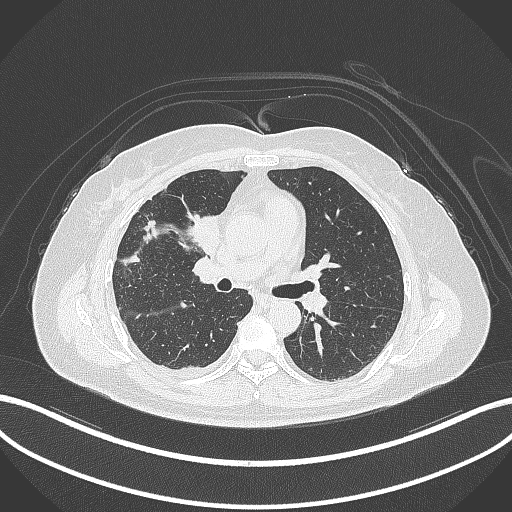
Chest CT, one axial slice; position 157 of 305 along the scan axis; 120 kVp; lung window (W 1500 / L -600 HU); 512 × 512 image matrix, field of view 400 × 400 mm. Female patient, age 52 years. Case-level facts recorded for this patient, not image findings: clinical TNM (as recorded): T3 N1 M1.
Outlined on this slice (rectangle marked by the reading radiologist):
- lung tumour (recorded histology: adenocarcinoma): bounding box (x1, y1, x2, y2) in pixels: (183, 208, 225, 258)